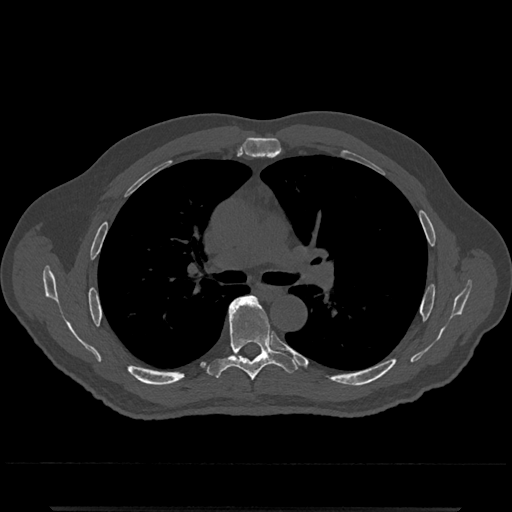
CT including the spine, one axial slice. Position 778 of 797 along the scan axis. Bone window (W 1800 / L 400 HU). 0.5 mm slice thickness. 512 × 512 image matrix, field of view 393 × 393 mm. Male patient, age 67 years. Case-level facts recorded for this patient, not image findings: primary cancer: prostate.
Structures marked on this image (semi-automatic segmentation, software-assisted and operator-edited):
- T5 vertebra: bounding box (x1, y1, x2, y2) in pixels: (254, 297, 256, 299)
- T6 vertebra: (207, 296, 298, 381)